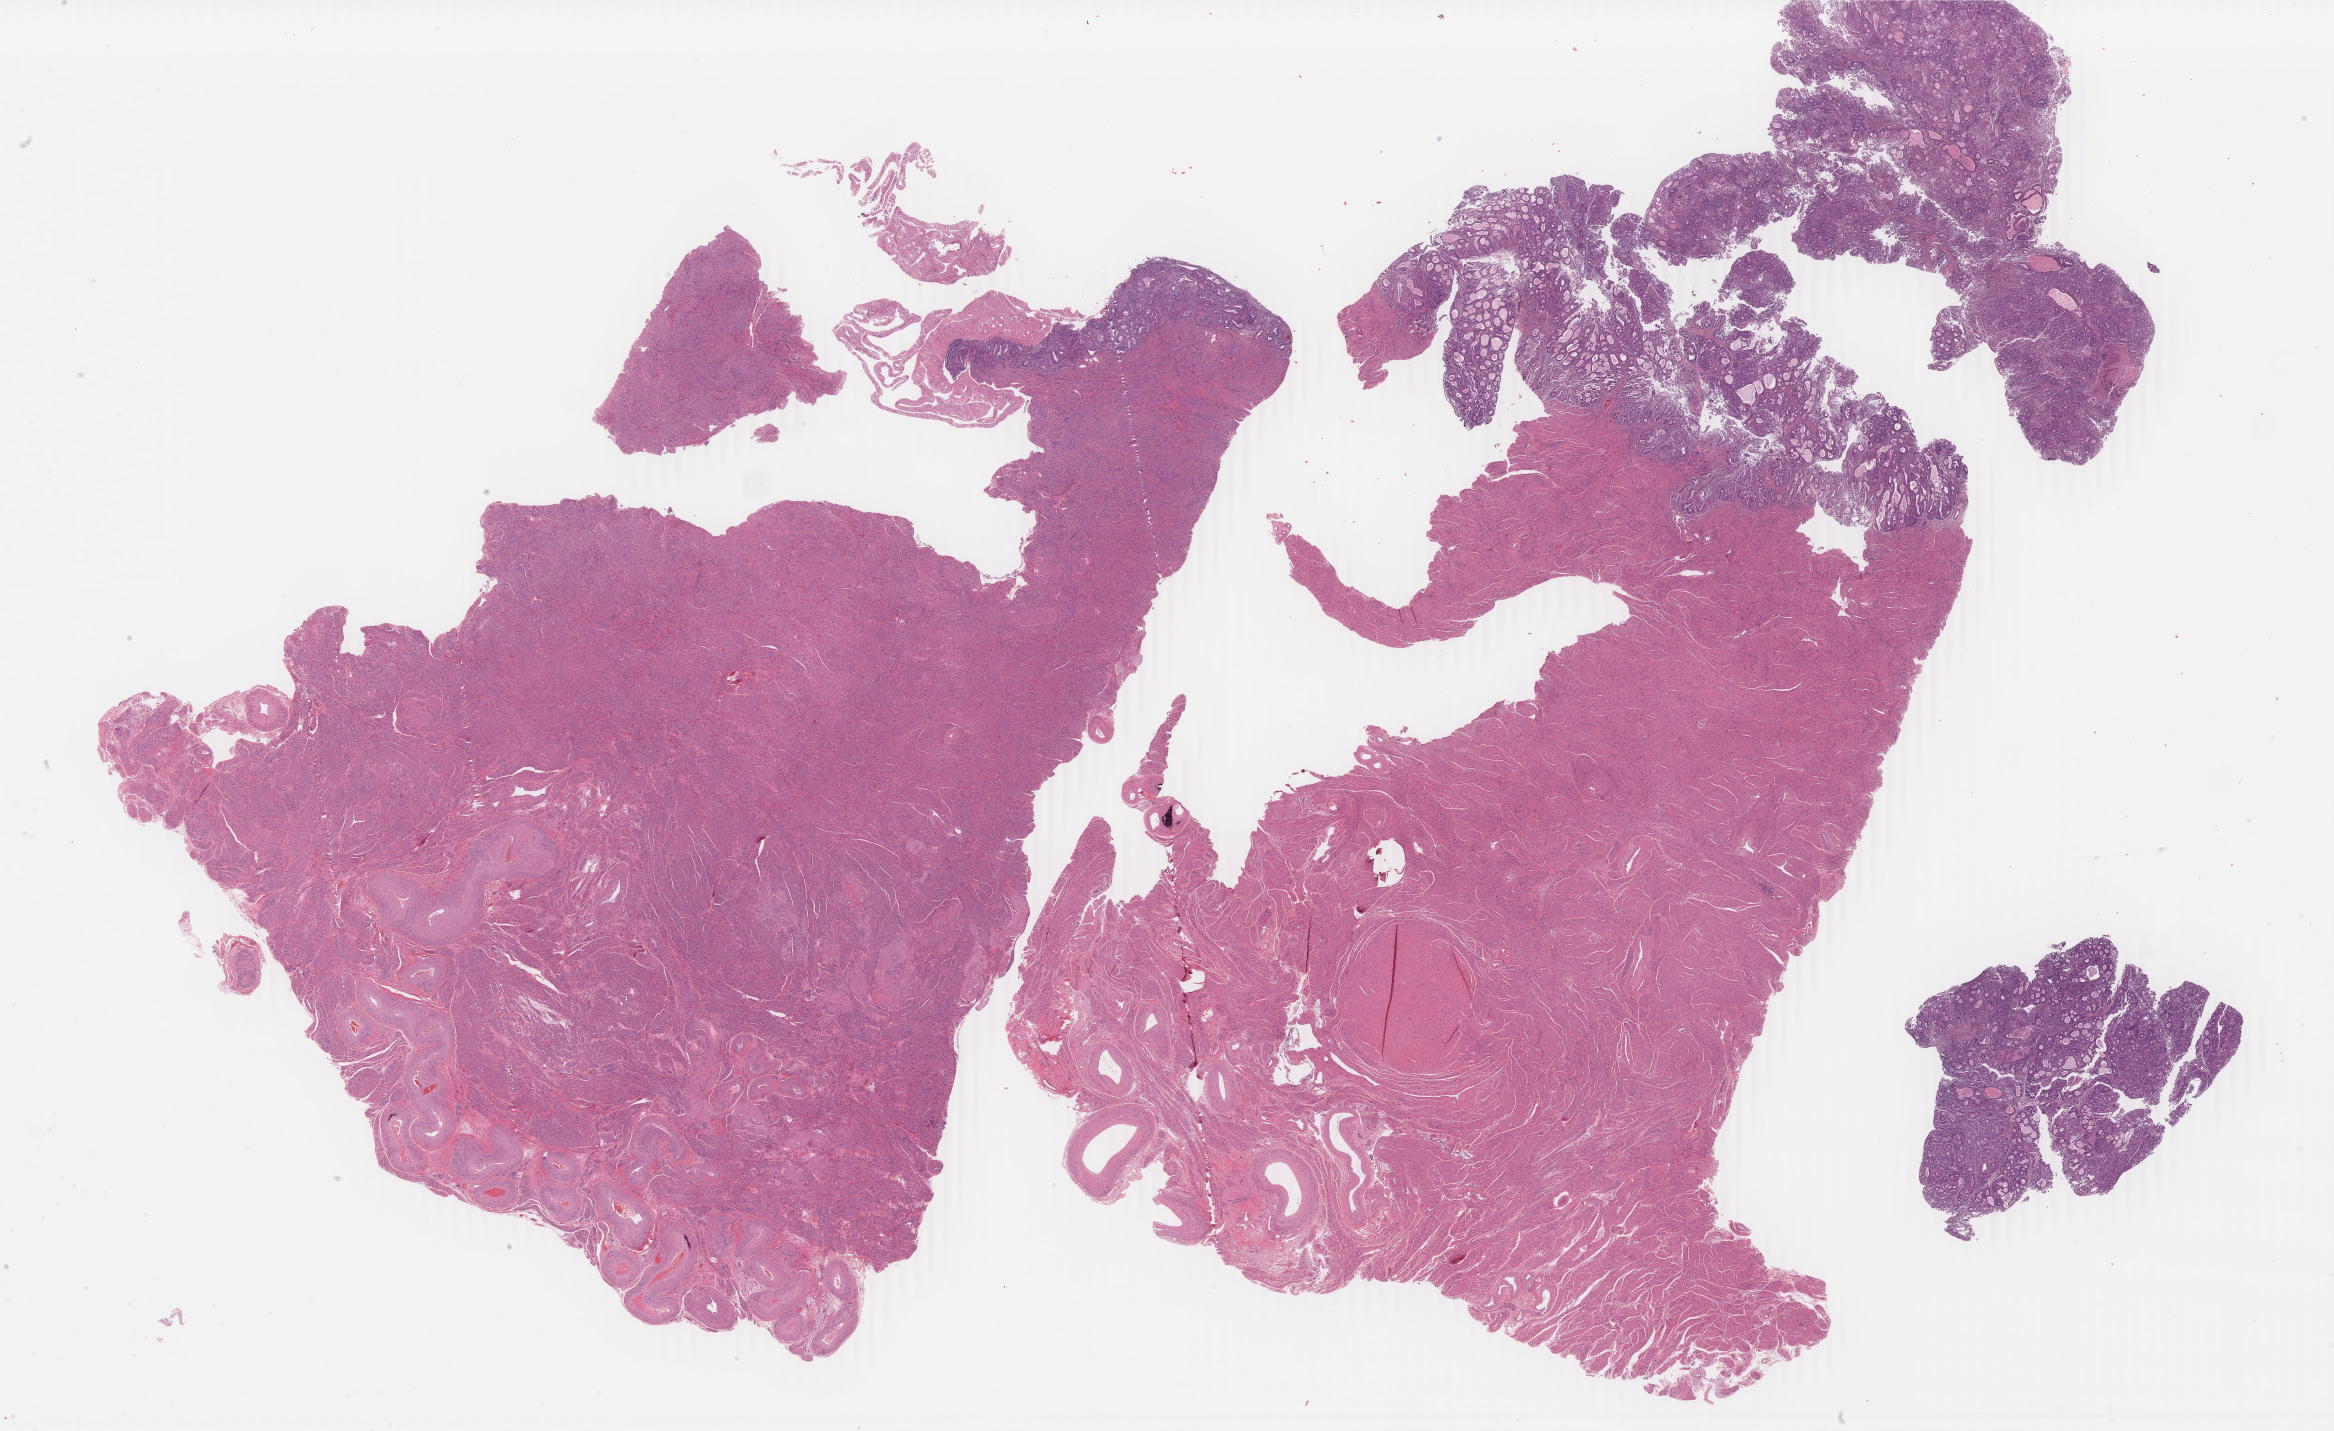
H&E-stained whole-slide image — shown as a low-resolution overview of the whole scanned area (about 37.1 x 22.8 mm, slide scanned at 40x), FFPE section, uterus, primary tumour sample. Patient: female, age at initial diagnosis 69 years. Histologic grade: G2 (moderately differentiated).
Diagnosis: Endometrioid adenocarcinoma, NOS (endometrium). FIGO stage: IB.